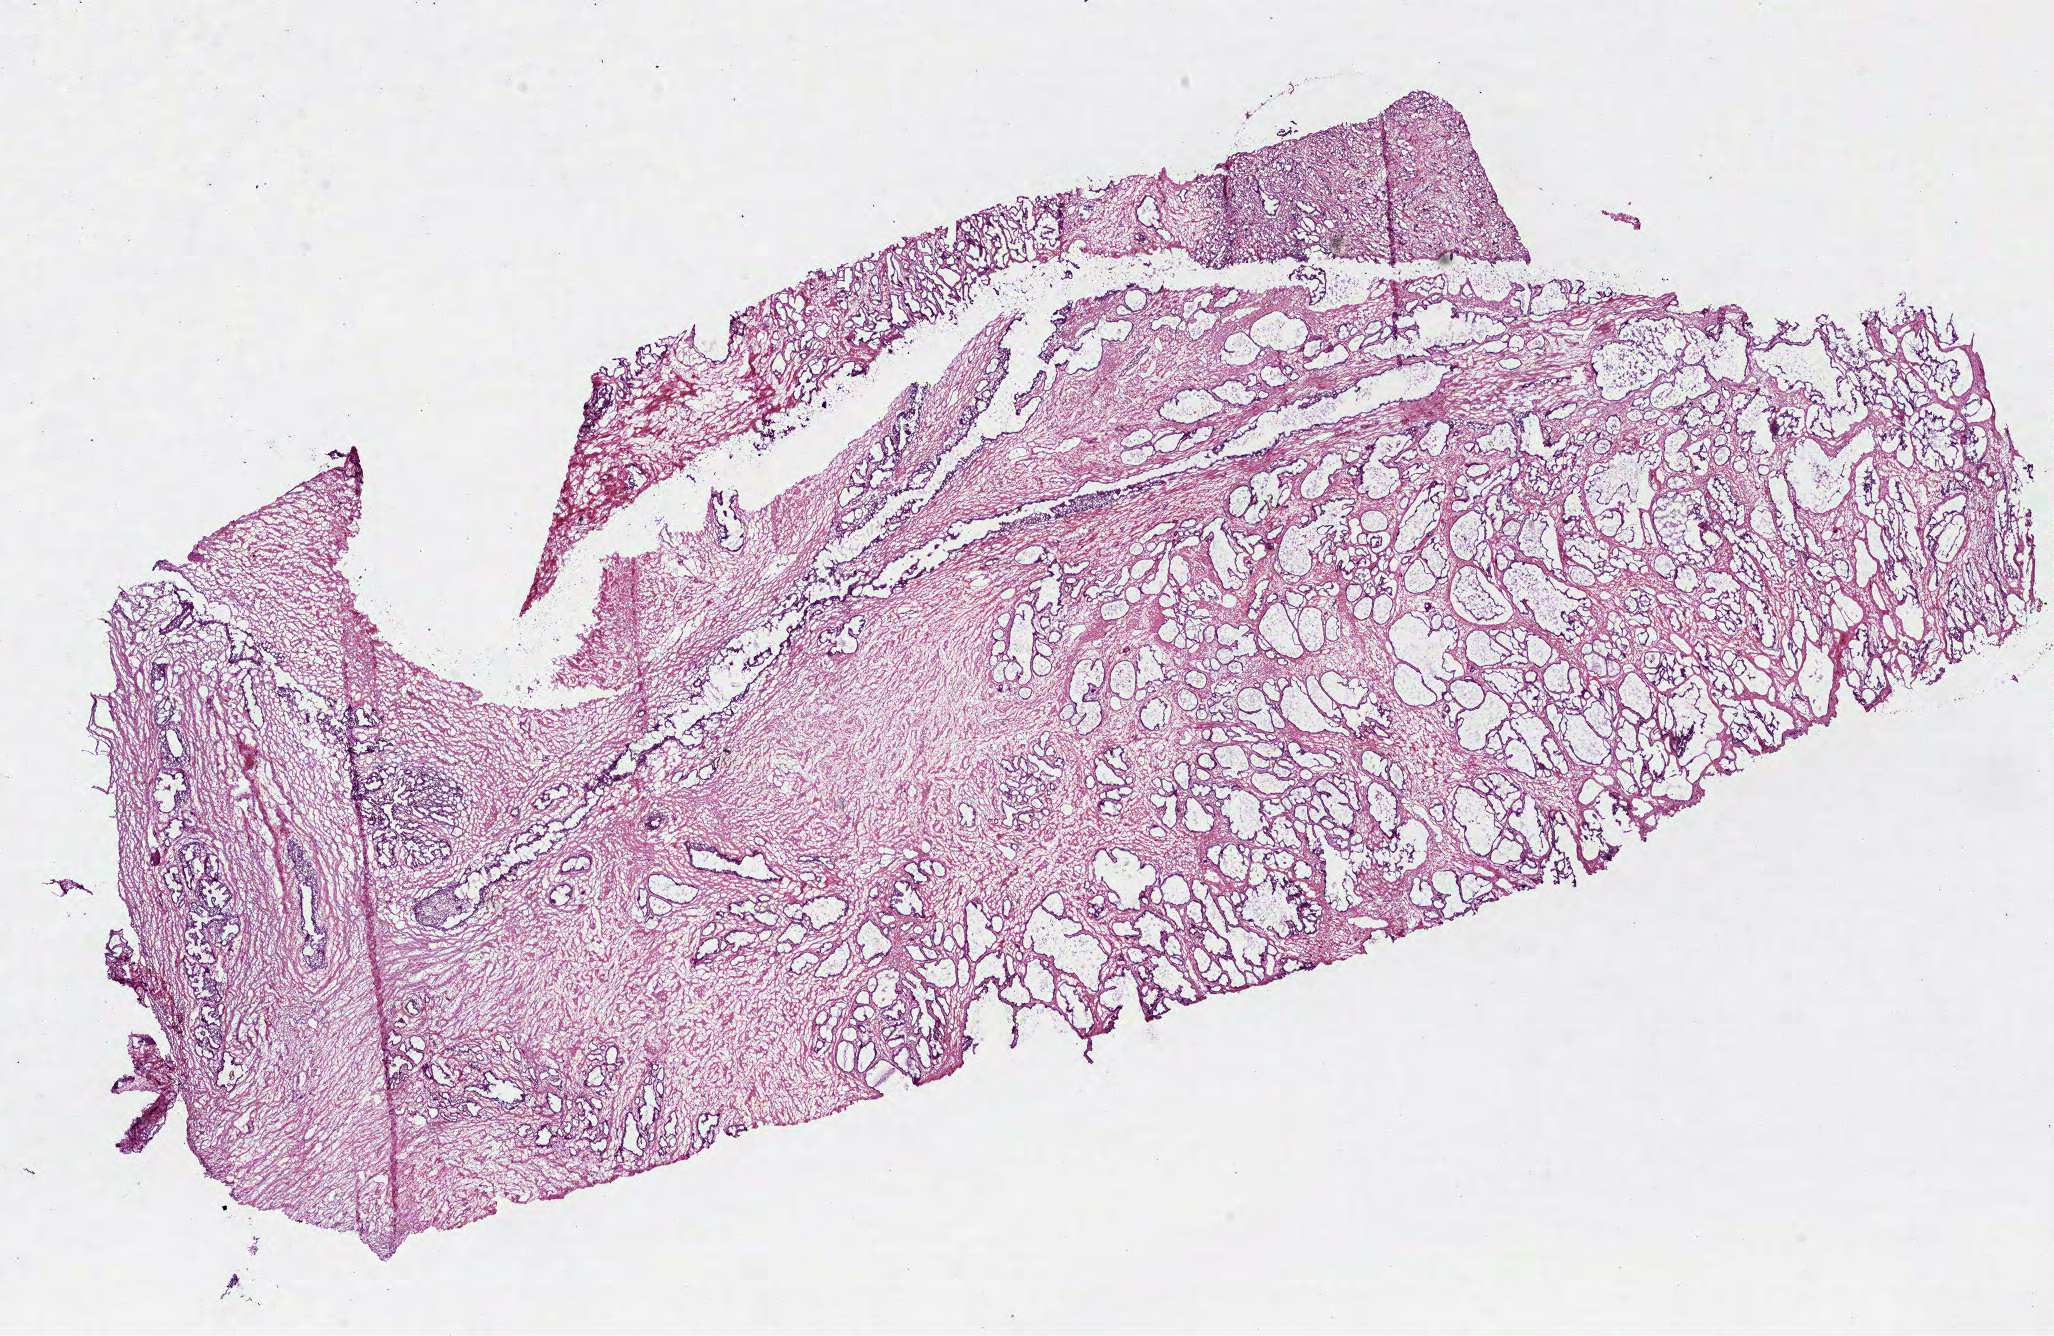
H&E whole-slide image — whole scanned area (about 16.6 x 10.8 mm) shown as a low-resolution overview; frozen section from the bottom of the tissue portion; sample: primary tumour, prostate. Male, age 60 years at initial diagnosis.
Histologic diagnosis: Acinar cell carcinoma (prostate gland).